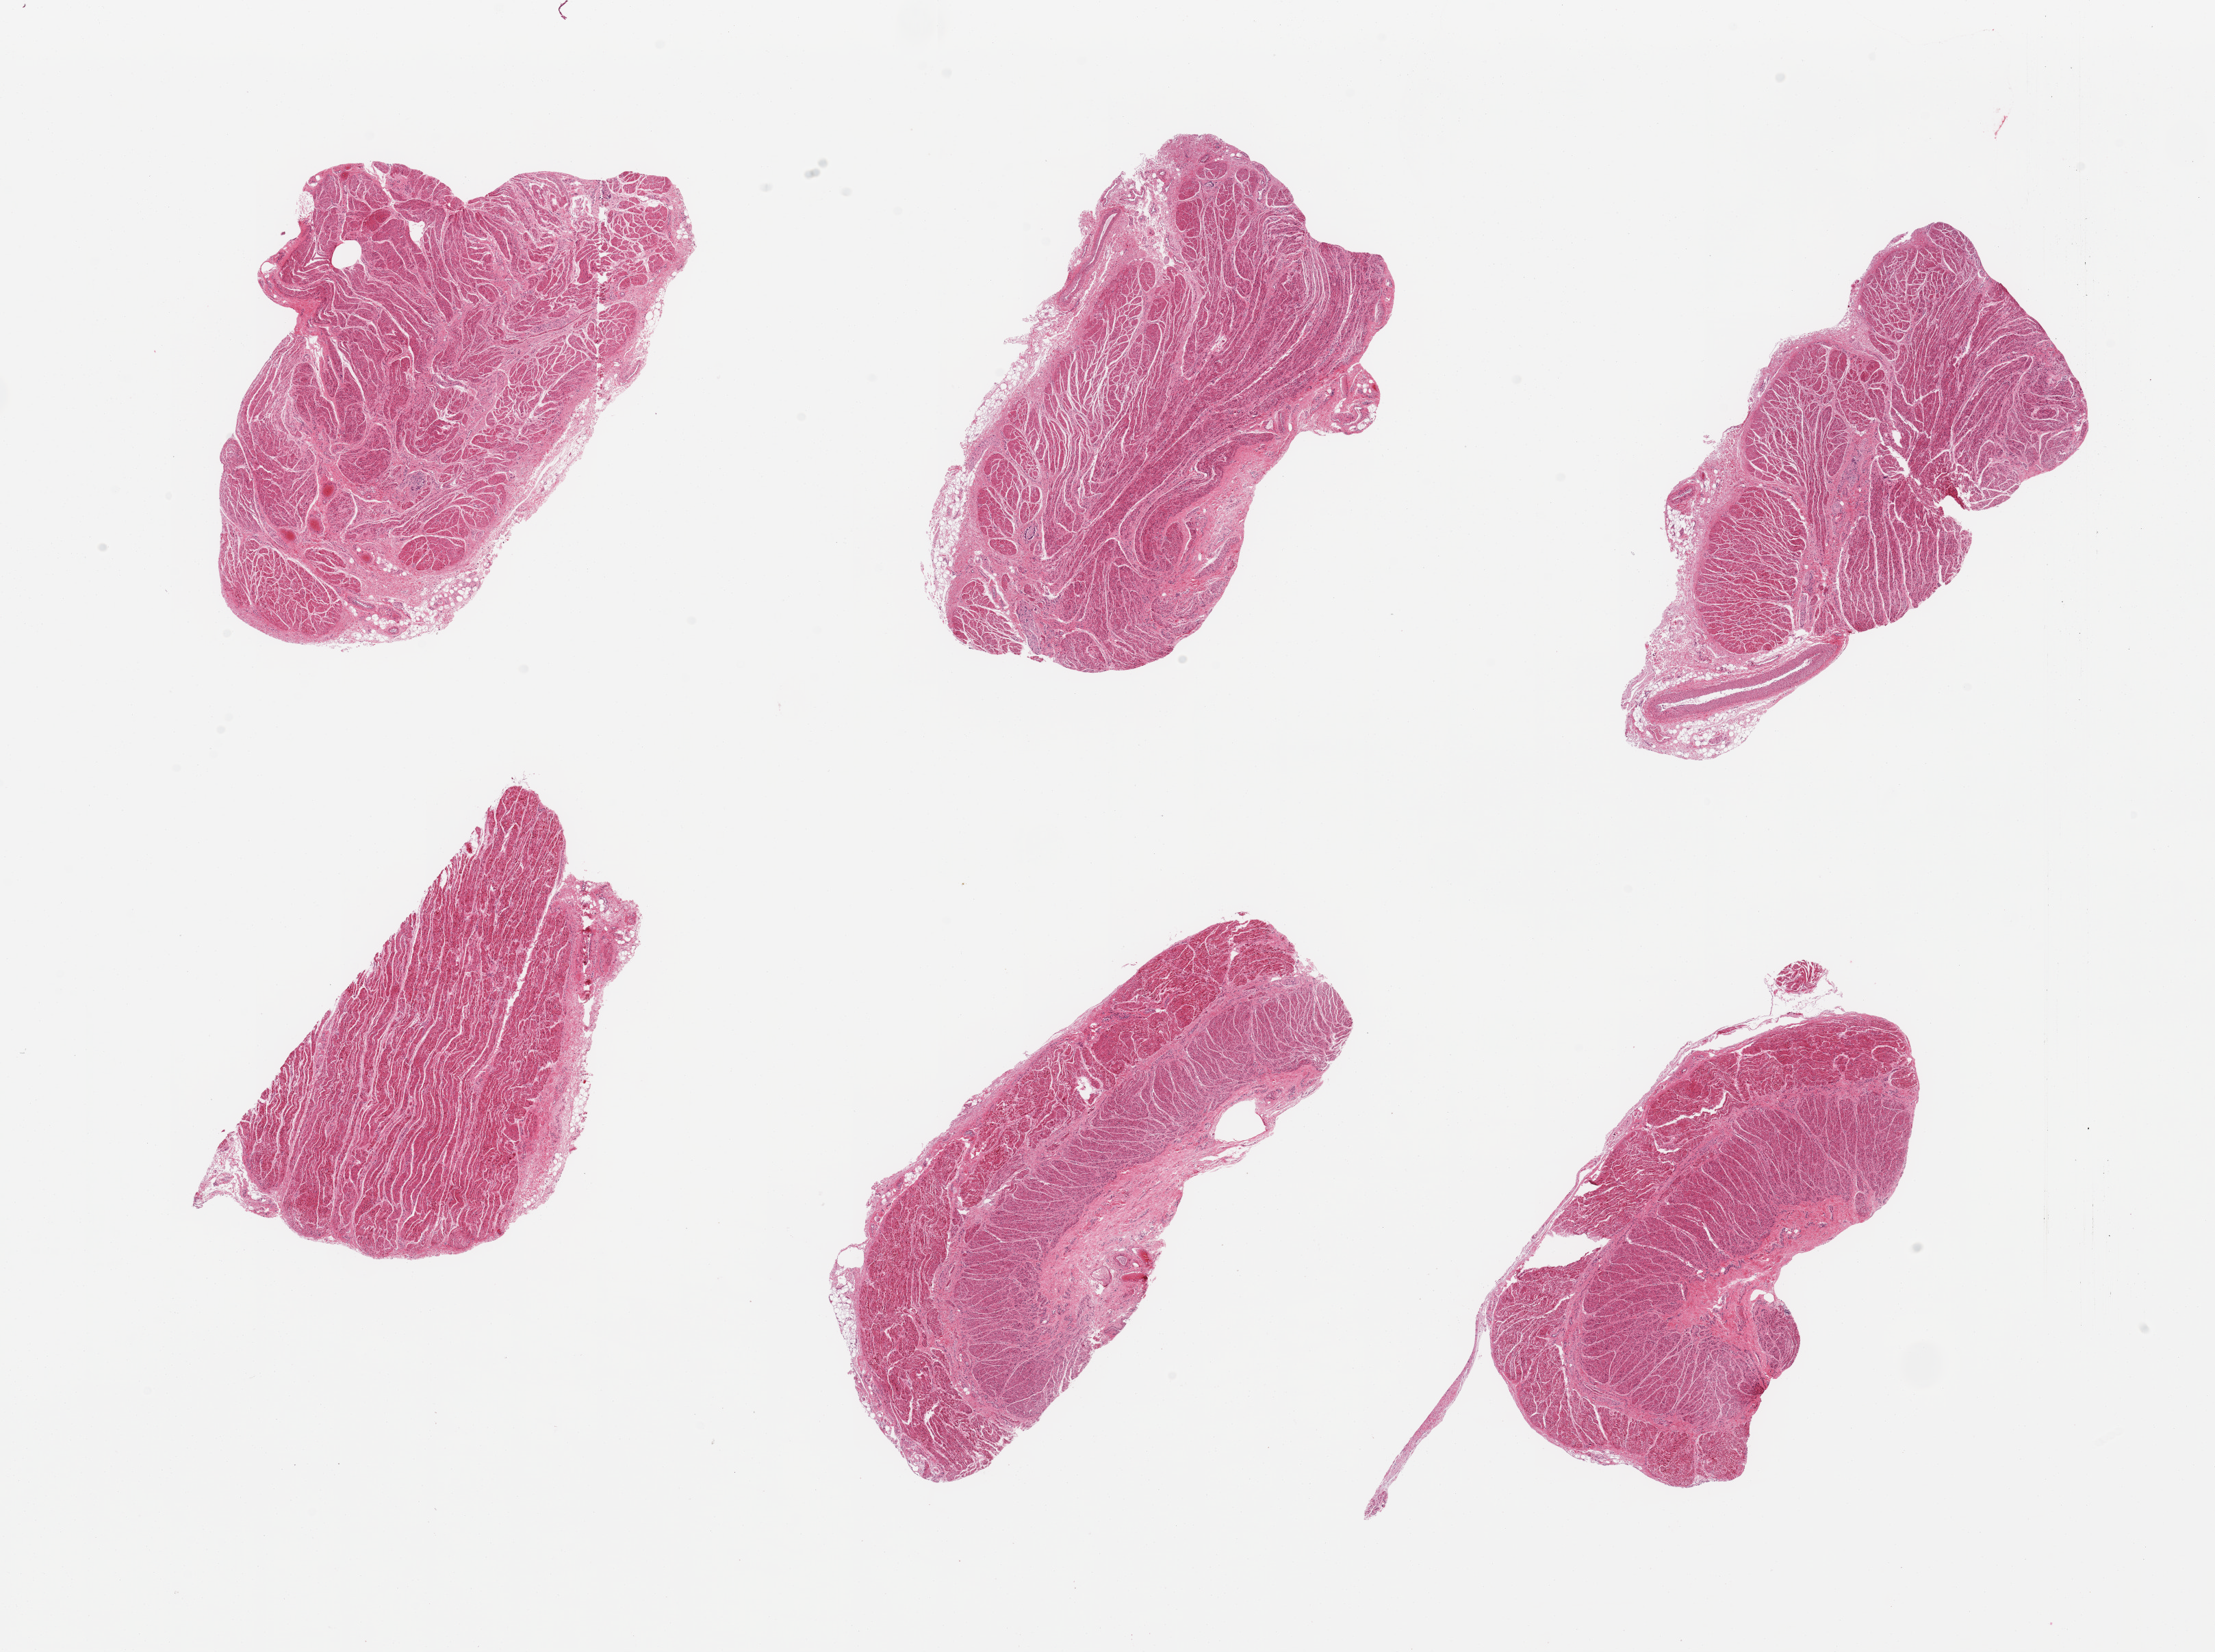
Digitized haematoxylin and eosin-stained section, shown as a low-resolution overview of the whole scanned area (about 25.6 x 19.1 mm, acquisition: 20x scan), PAXgene-fixed paraffin-embedded (PFPE) section, section of gastroesophageal junction (target tissue), tissue donor sample. Male donor.
Reviewer comment on this tissue sample: 2 pieces, confirmed target muscularis.